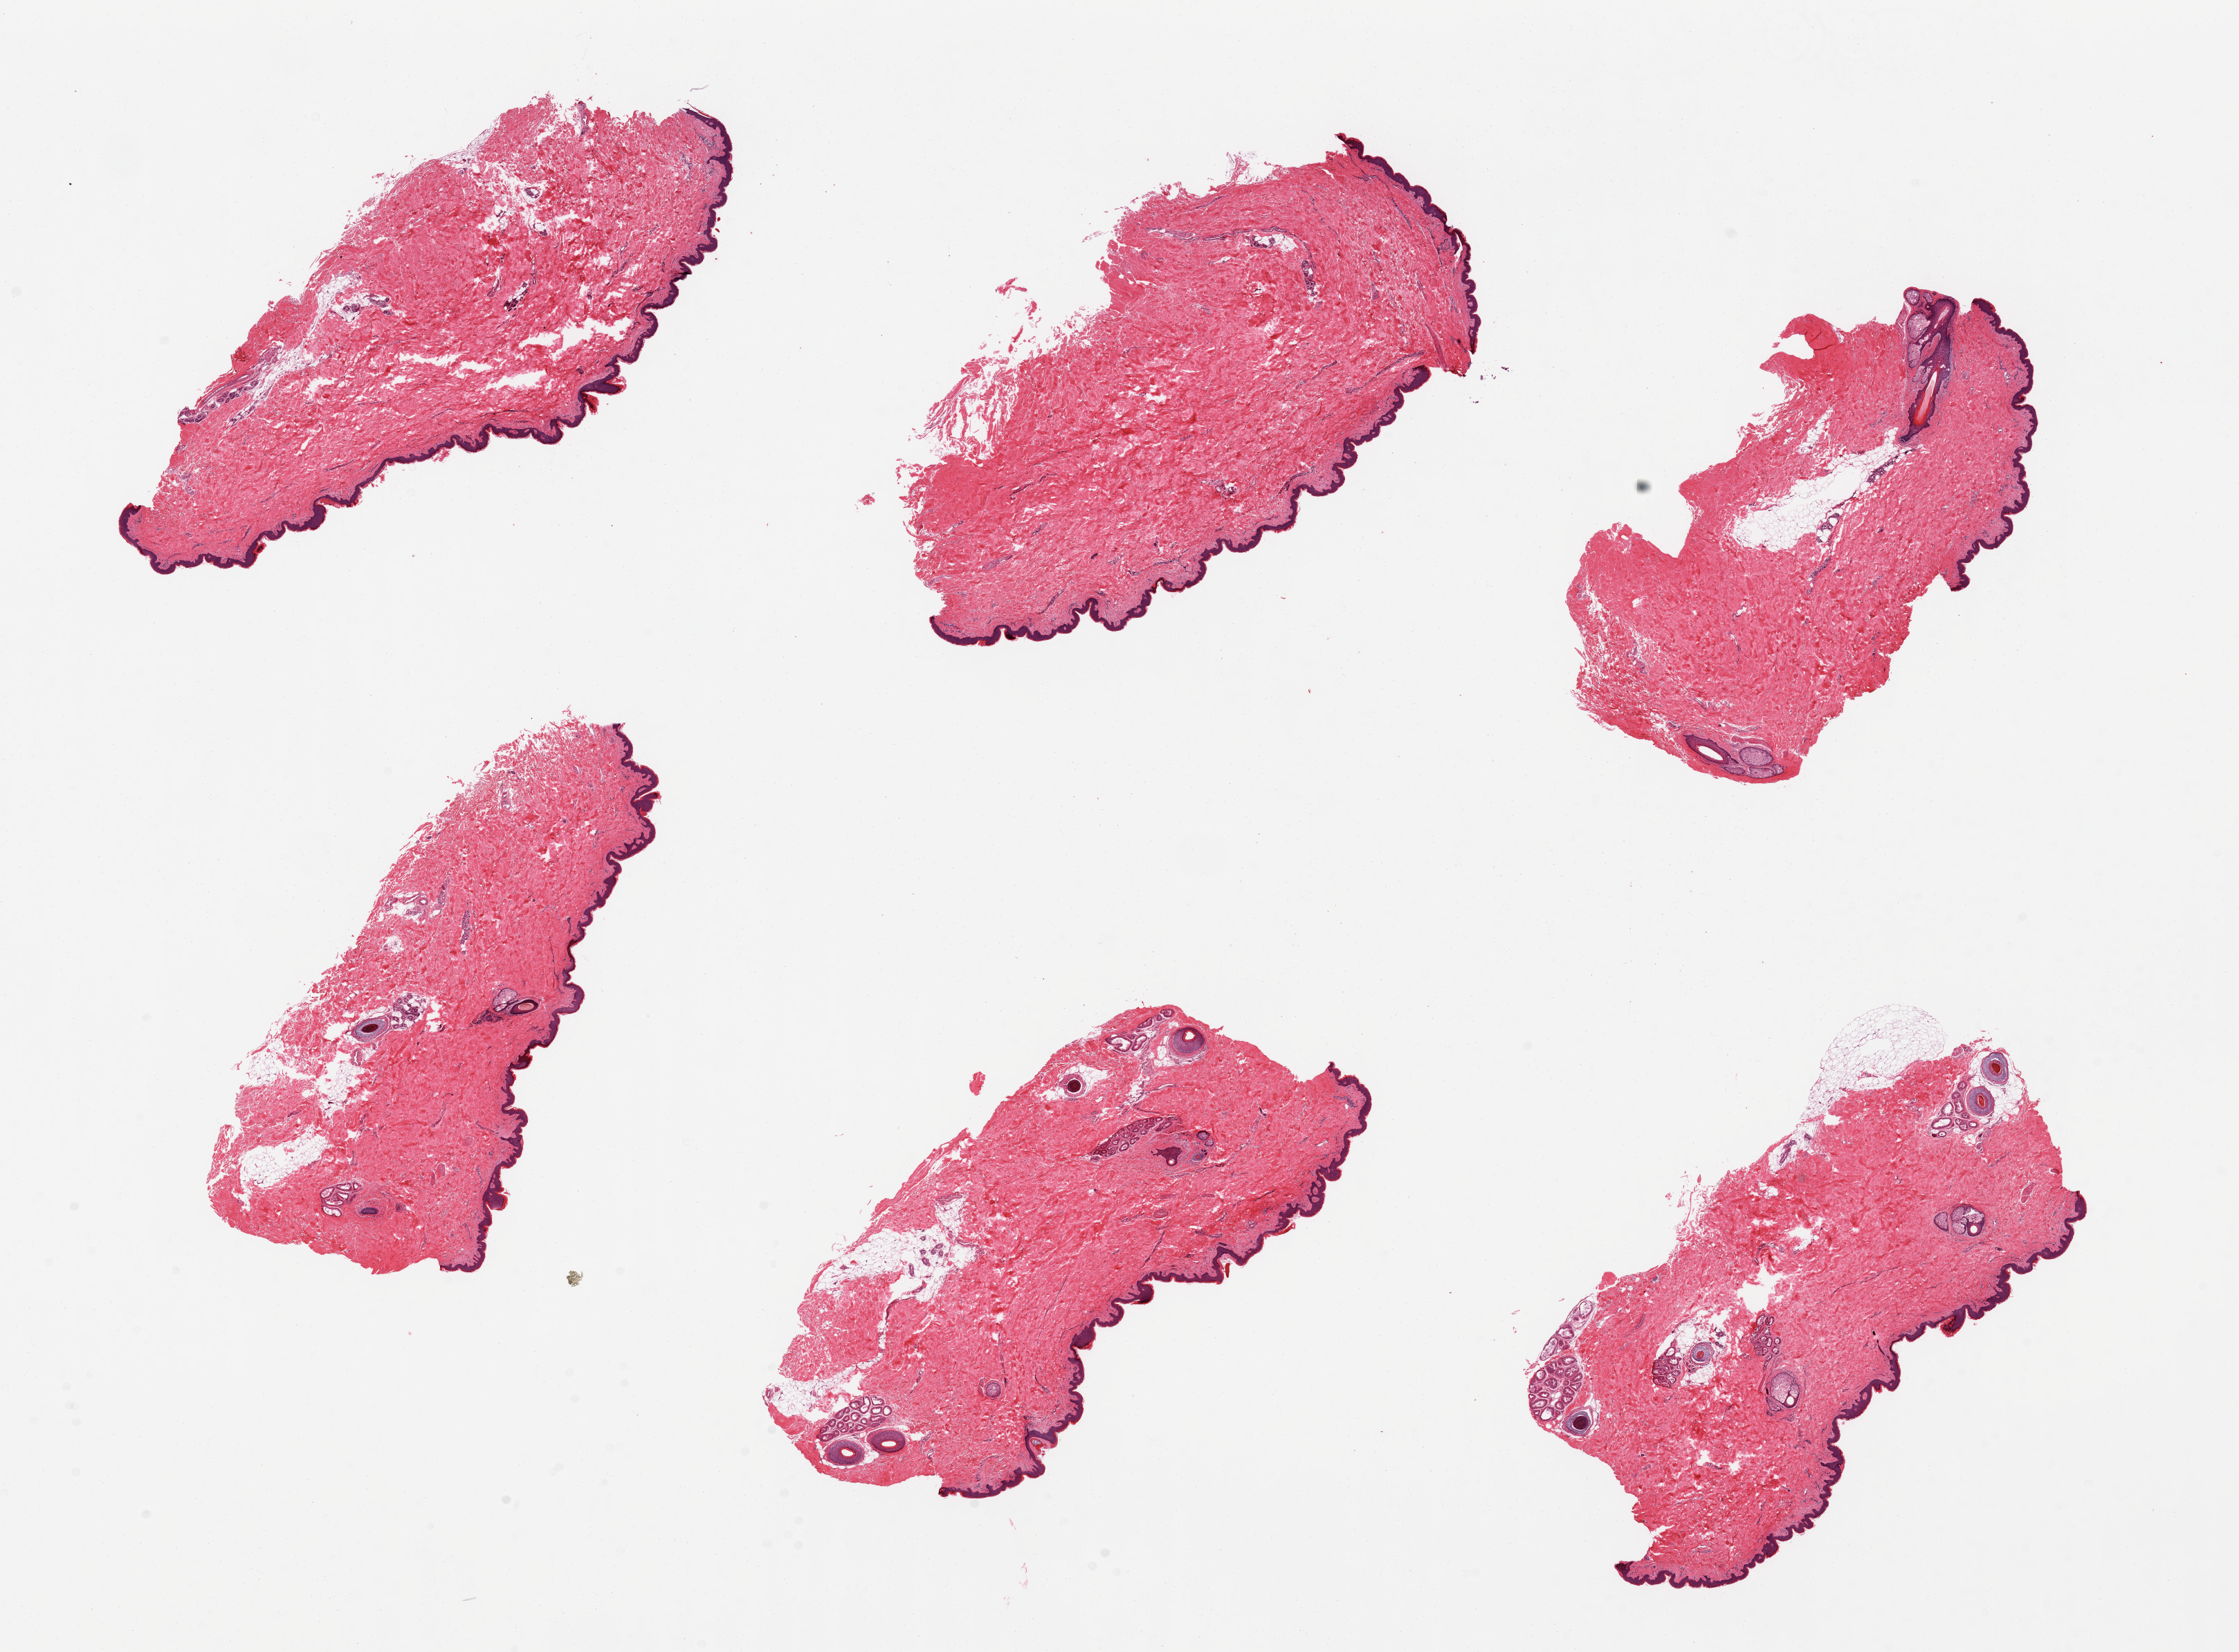
Whole-slide image, hematoxylin and eosin (H&E) stain, brightfield — low-resolution overview of the scanned area, about 25.6 x 18.9 mm, PAXgene-fixed paraffin-embedded (PFPE) section, target tissue: skin of suprapubic region, donor tissue sample.
Pathologist's review note for this sample: 6 pieces; well; trimmed; contains 10% internal fat.